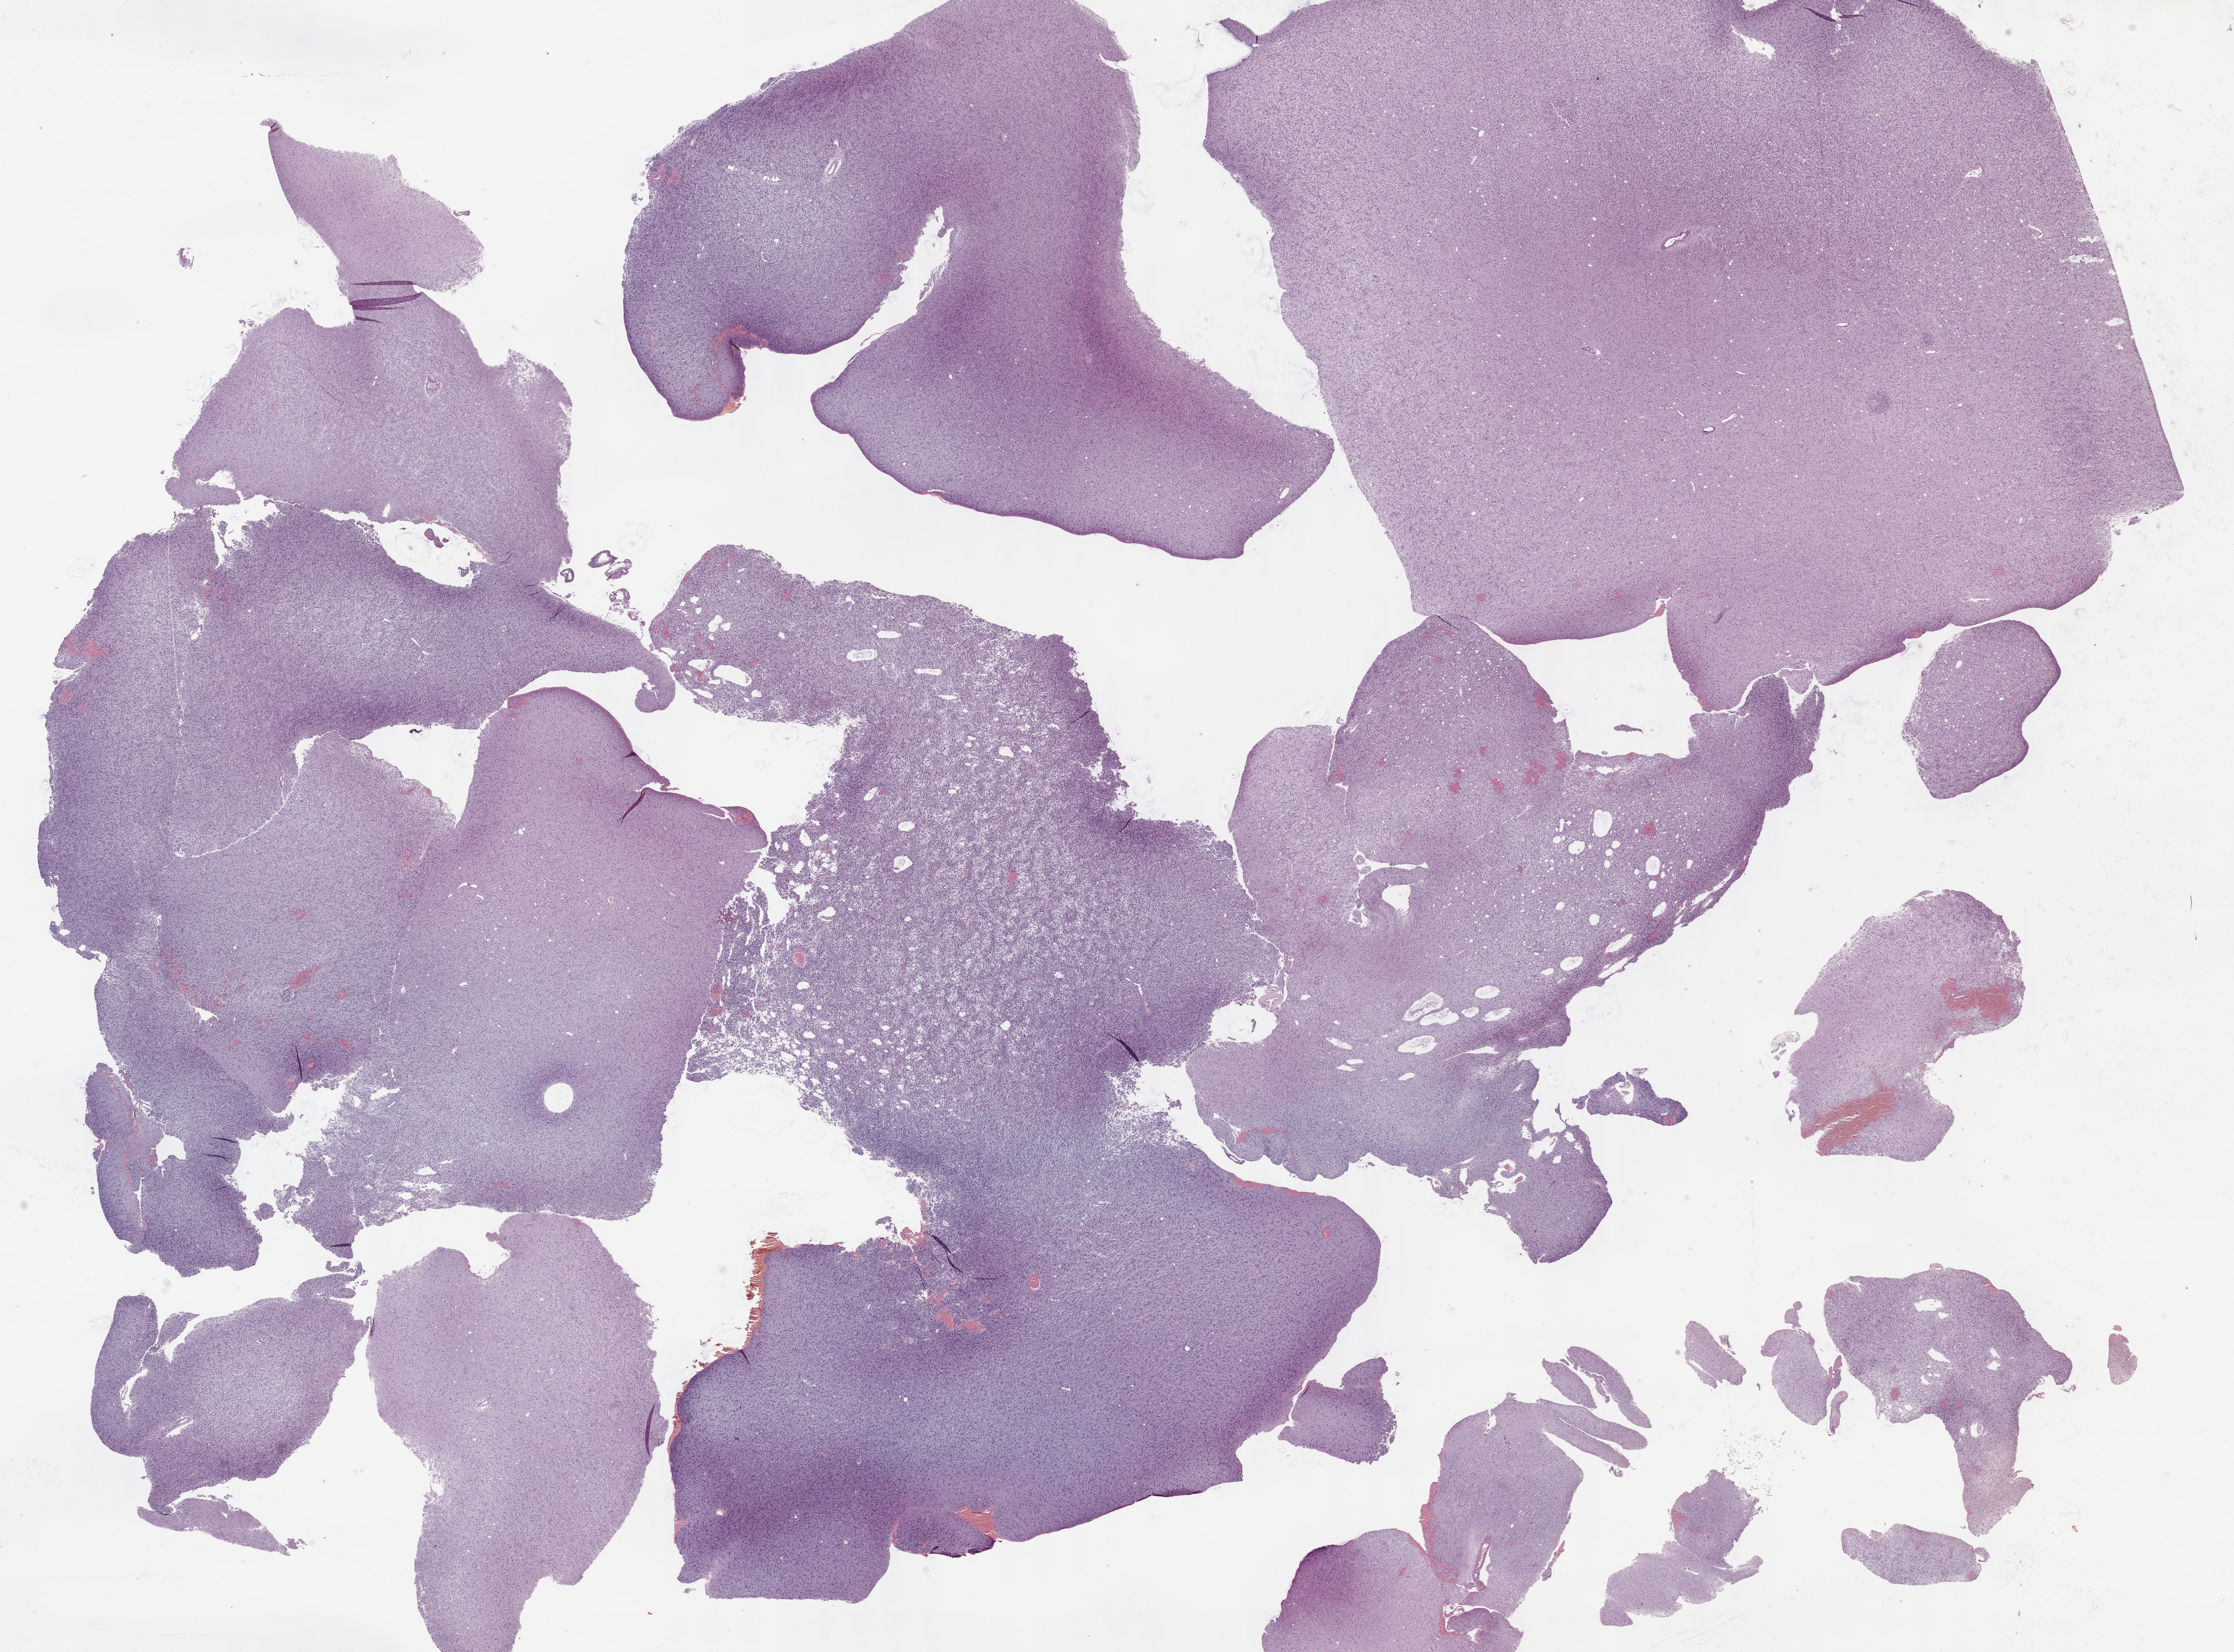
Hematoxylin and eosin (H&E) stained whole-slide image — whole scanned area (about 30.7 x 22.7 mm) shown as a low-resolution overview. FFPE section. Brain, primary tumour sample. Male, age 35 years at initial diagnosis. Histologic grade: G3 (poorly differentiated).
Pathologic diagnosis: Astrocytoma, anaplastic (cerebrum).